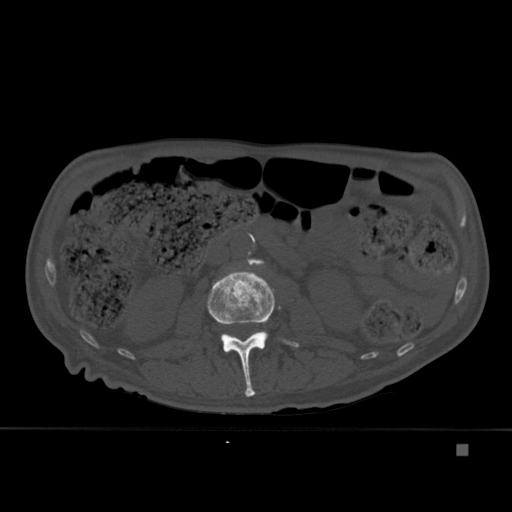
CT including the spine, one axial slice. Position 159 of 451 along the scan axis. Bone window (W 1800 / L 400 HU). 1.5 mm slice thickness. 512 × 512 image matrix, field of view 378 × 378 mm. Male patient, age 75 years. Case-level facts recorded for this patient, not image findings: primary cancer: prostate.
Structures marked on this image (semi-automatic segmentation, software-assisted and operator-edited):
- L2 vertebra: bounding box (x1, y1, x2, y2) in pixels: (207, 268, 299, 397)
- L3 vertebra: (247, 259, 265, 266)